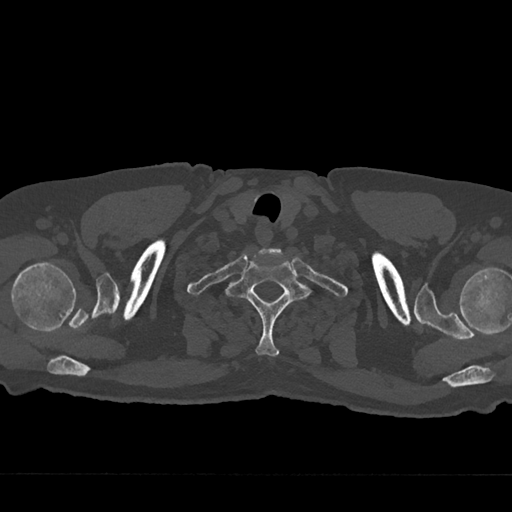
CT including the spine, one axial slice. Position 658 of 797 along the scan axis. 120 kVp. Bone window (W 1800 / L 400 HU). 0.5 mm slice thickness. 512 × 512 image matrix. Male patient, age 75 years. Case-level facts recorded for this patient, not image findings: primary cancer: renal; vertebrae with lytic lesions (as recorded): T4.
Outlined on this slice (semi-automatic segmentation, software-assisted and operator-edited):
- T1 vertebra: bounding box [x1, y1, x2, y2] px = [224, 253, 313, 357]
- T2 vertebra: [278, 293, 284, 299]